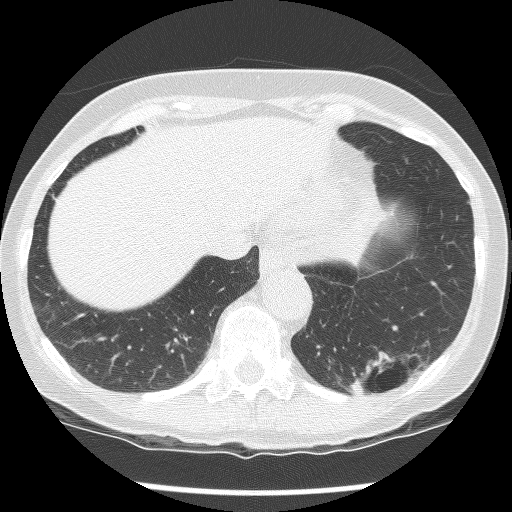
Low-dose screening chest CT, axial slice; second annual screen; lung window (W 1500 / L -600 HU); 2.5 mm slice thickness; slice 102 of 136 in the series; 512 × 512 image matrix, field of view 300 × 300 mm. Female, age 61 years at enrolment. Current smoker at enrolment.
Expert-annotated lung lesion, box from (x=328, y=313) to (x=440, y=413) px. The screening reader recorded 2 non-calcified nodules or masses ≥4 mm on this exam; which of them this box marks is not recorded. Participant outcome: lung cancer diagnosed 585 days after this screen (after the third annual screen) — non-small cell carcinoma, left lower lobe, poorly differentiated (G3), stage IB (AJCC 6th edition), 100 mm at pathology.